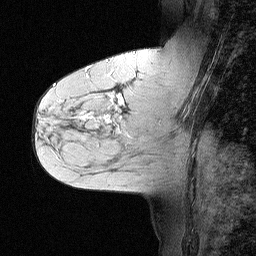
Breast MRI (dynamic contrast-enhanced), one sagittal slice; slice 28 of 64 in the series (ordered by position); dynamic contrast-enhanced study with each time point stored as its own series, time point 2 of 3 at this slice position (early post-contrast, ordered by acquisition time); 1.5 T; TE 4.5 ms, TR 11 ms; 256 × 256 image matrix. Female patient, age 55 years. From the clinical record (not read from this slice): setting: breast cancer imaged before/during neoadjuvant chemotherapy; receptor status: triple-negative.
Structures marked on this image (semi-automatically segmented with operator editing):
- analysis volume of interest (the breast-tissue region the enhancement analysis was run in; not a lesion): box from (x=71, y=63) to (x=147, y=145) px
- tumour enhancement mask (voxels above the 90 % enhancement threshold inside the analysis volume of interest): (x=81, y=94)–(x=121, y=123)